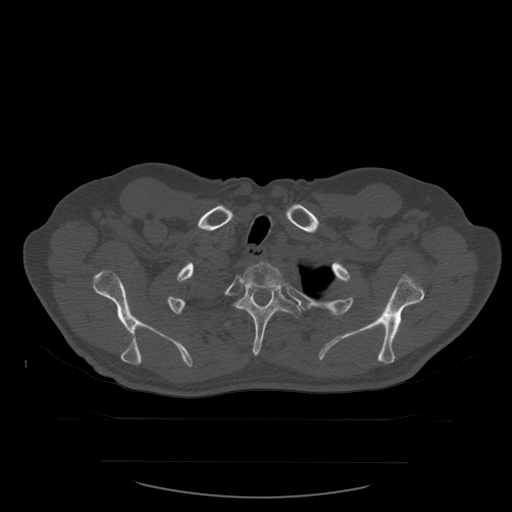
CT including the spine, one axial slice; position 462 of 590 along the scan axis; bone window (W 1800 / L 400 HU); 1.25 mm slice thickness; 512 × 512 image matrix, field of view 479 × 479 mm. Patient age 71 years. Case-level facts recorded for this patient, not image findings: primary cancer: lung.
Structures marked on this image (semi-automatic segmentation, software-assisted and operator-edited):
- T2 vertebra: bounding box [x1, y1, x2, y2] px = [243, 262, 286, 289]
- T3 vertebra: [235, 288, 302, 357]
- T4 vertebra: [225, 322, 233, 329]